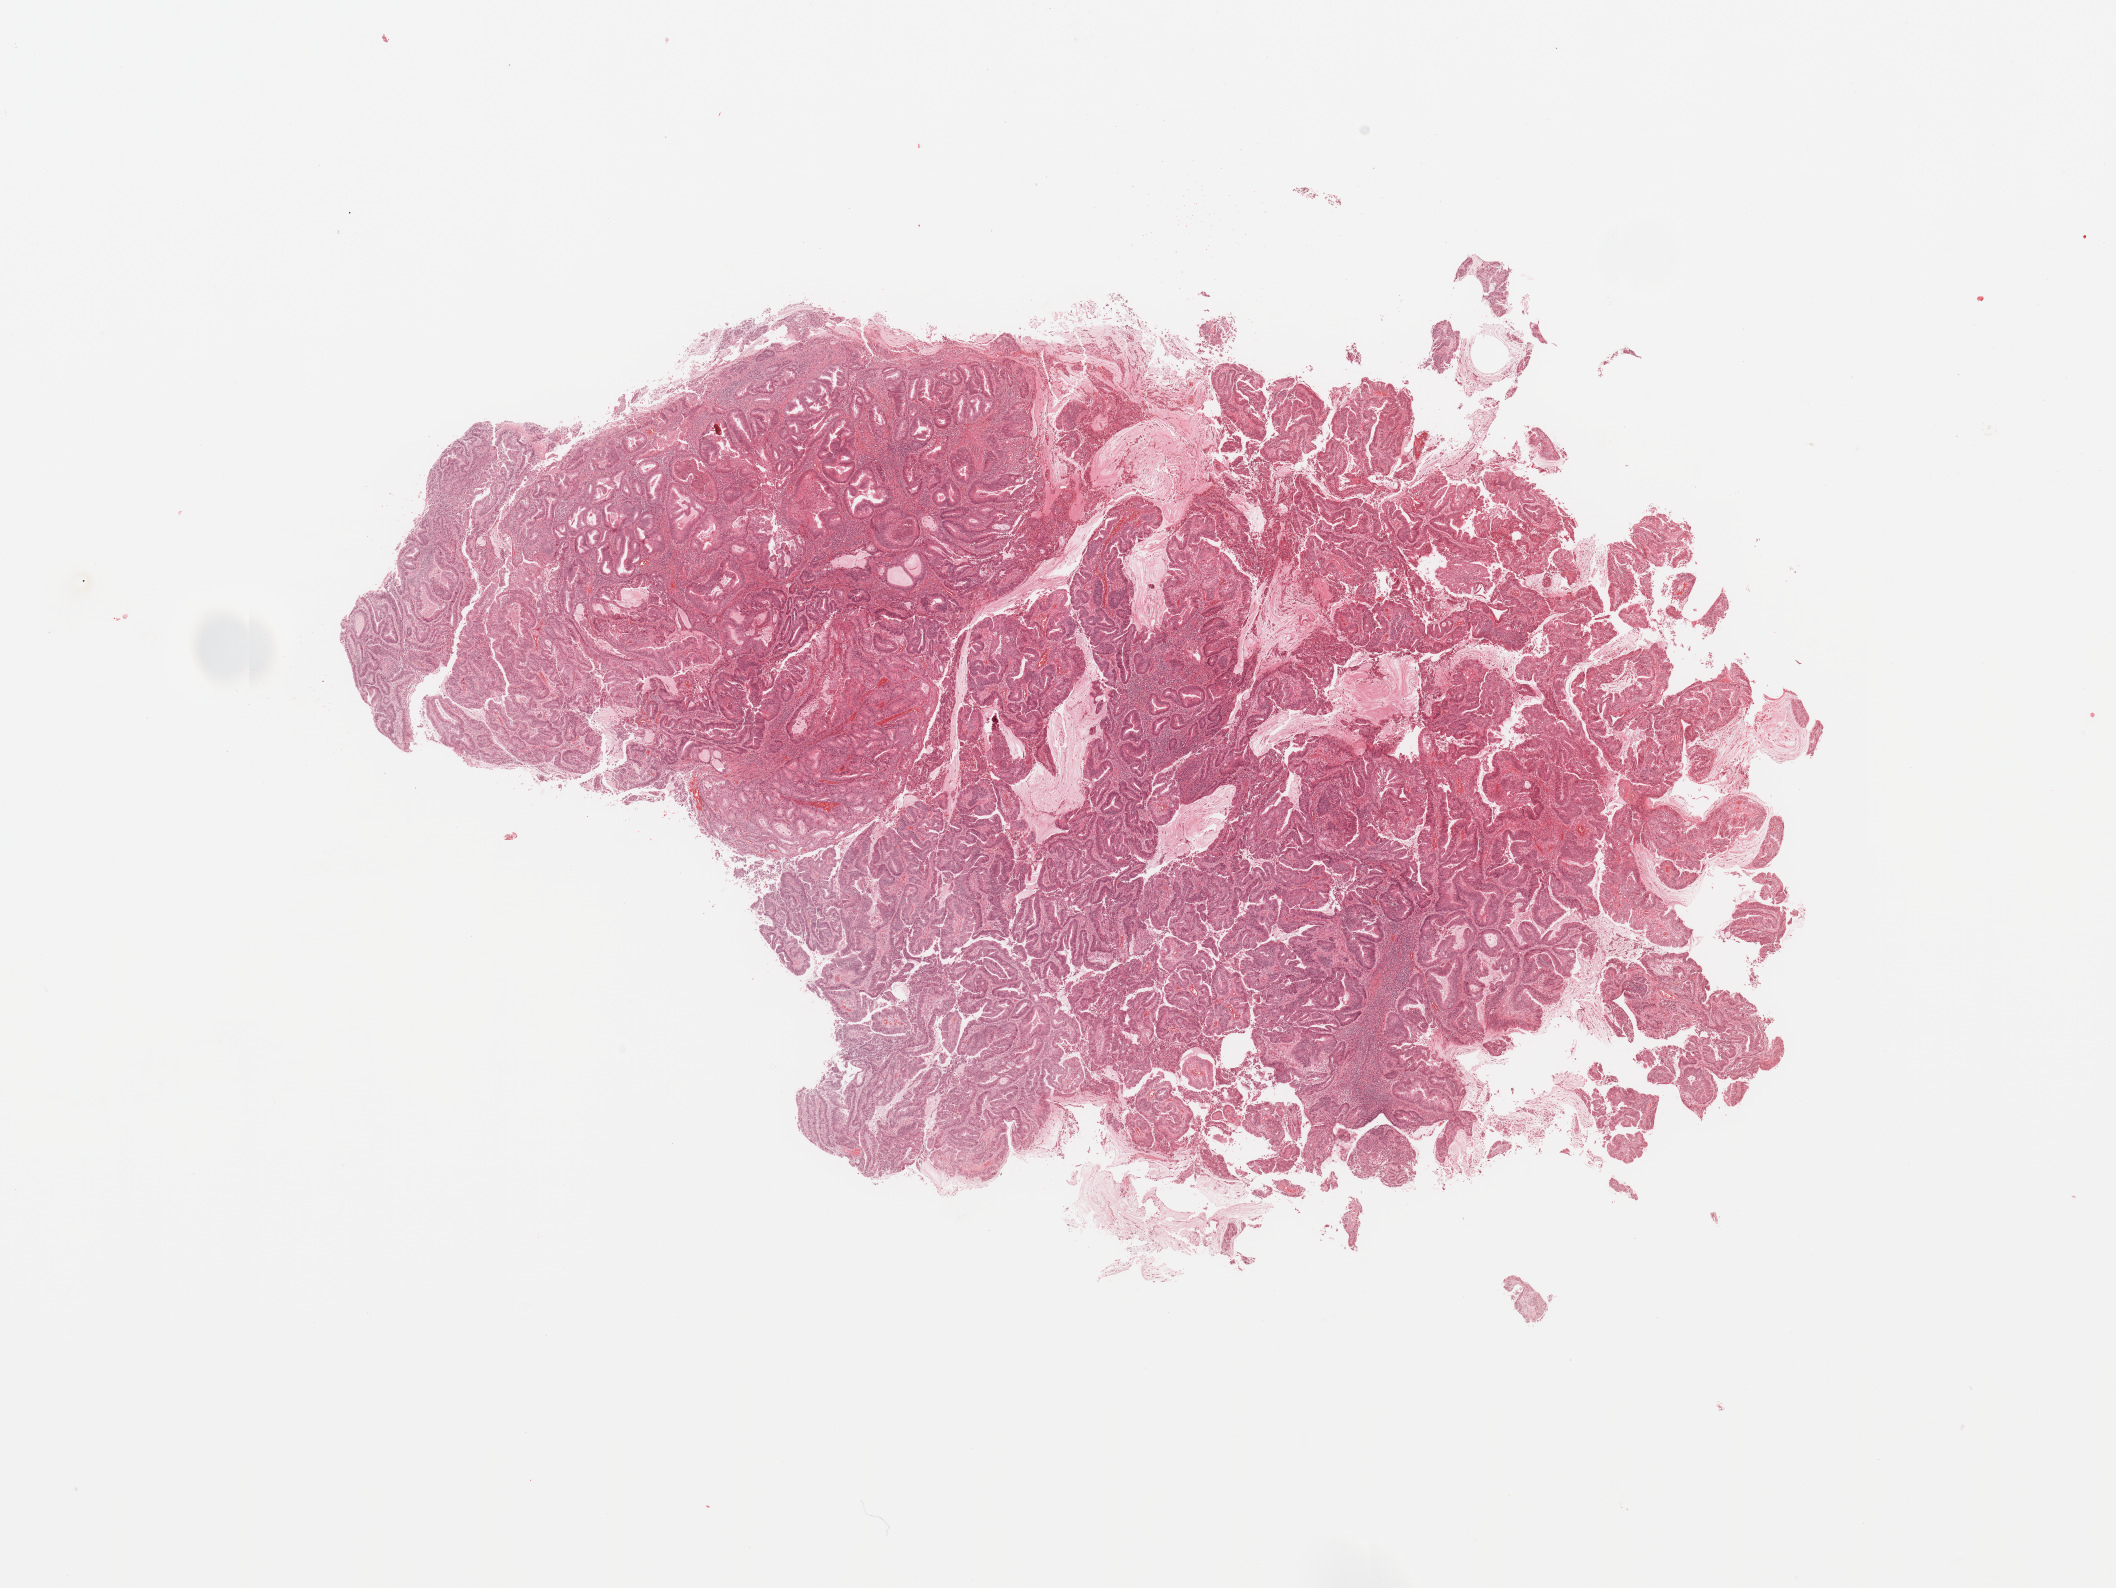
Digitized H&E-stained tissue section (whole slide) — low-resolution overview of the scanned area, about 16.7 x 12.6 mm (slide scanned at 20x), tumour tissue sample, sampled site: uterus. Female, 73 y/o. Histologic grade: G2 (moderately differentiated). Pathologist review of this section (percent, as recorded): tumour nuclei 90%, necrosis 5%.
- AJCC pathologic stage: I
- primary tumour site (as recorded): anterior endometrium
- diagnosis: Endometrioid adenocarcinoma, NOS